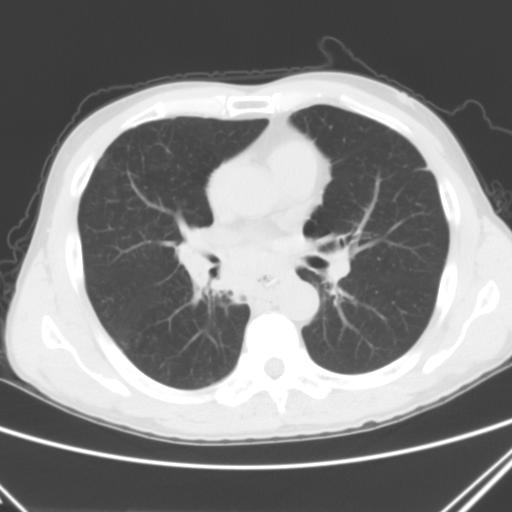
Chest CT, one axial slice. Position 25 of 51 along the scan axis. Lung window (W 1500 / L -600 HU). 512 × 512 image matrix, field of view 327 × 327 mm. Patient: male, 52 years. From the clinical record (not read from this slice): clinical TNM (as recorded): T2a N0 M1c.
Structures marked on this image (rectangle marked by the reading radiologist):
- lung tumour (recorded histology: squamous cell carcinoma): bounding box (x1, y1, x2, y2) in pixels: (165, 217, 245, 319)